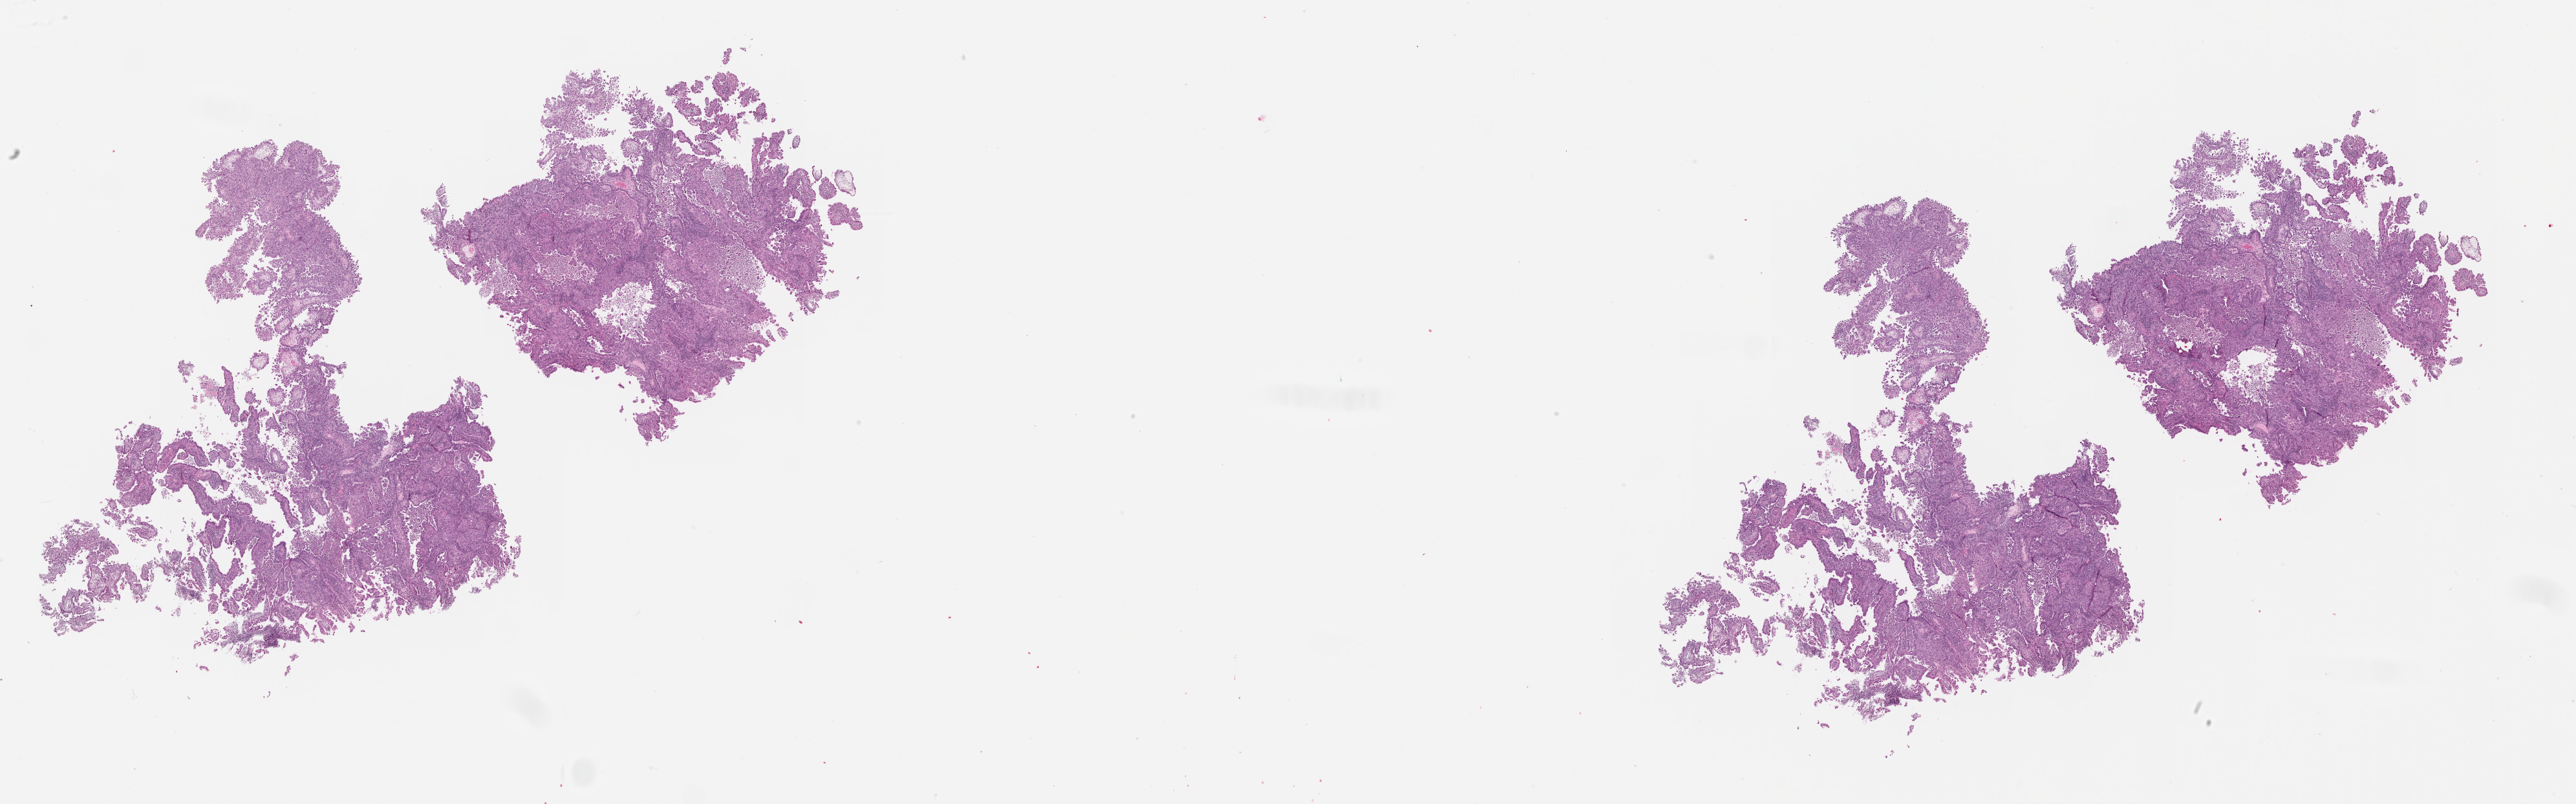
H&E whole-slide image — low-resolution overview of the scanned area, about 32.1 x 10.0 mm (slide scanned at 20x); uterus, tissue type not recorded.
Patient diagnosis (cohort enrolment): corpus endometrial carcinoma (uterus).